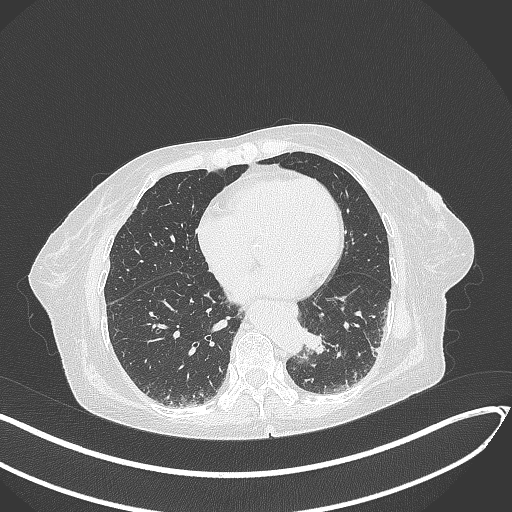
Chest CT, one axial slice; lung window (W 1500 / L -600 HU); 1 mm slice thickness; 512 × 512 image matrix. Patient: female, 82 years. From the clinical record (not read from this slice): clinical TNM (as recorded): T1b N0 M1.
Outlined on this slice (bounding box drawn by a radiologist):
- lung tumour (recorded histology: adenocarcinoma): box from (x=298, y=324) to (x=332, y=360) px